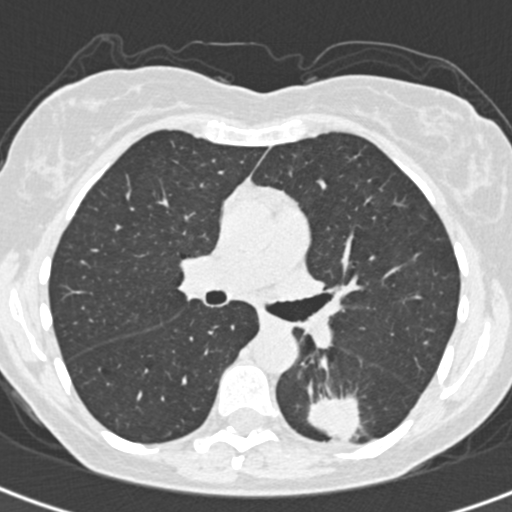
Low-dose screening chest CT, one axial slice. Position 200 of 328 along the scan axis. 120 kVp. Lung window (W 1500 / L -600 HU). 1 mm slice thickness. 512 × 512 image matrix, field of view 284 × 284 mm.
Outlined on this slice (manually delineated by an expert):
- lesion 1 (tumor, lower lobe of left lung): bounding box <307,395,361,441> (left, top, right, bottom; pixels)